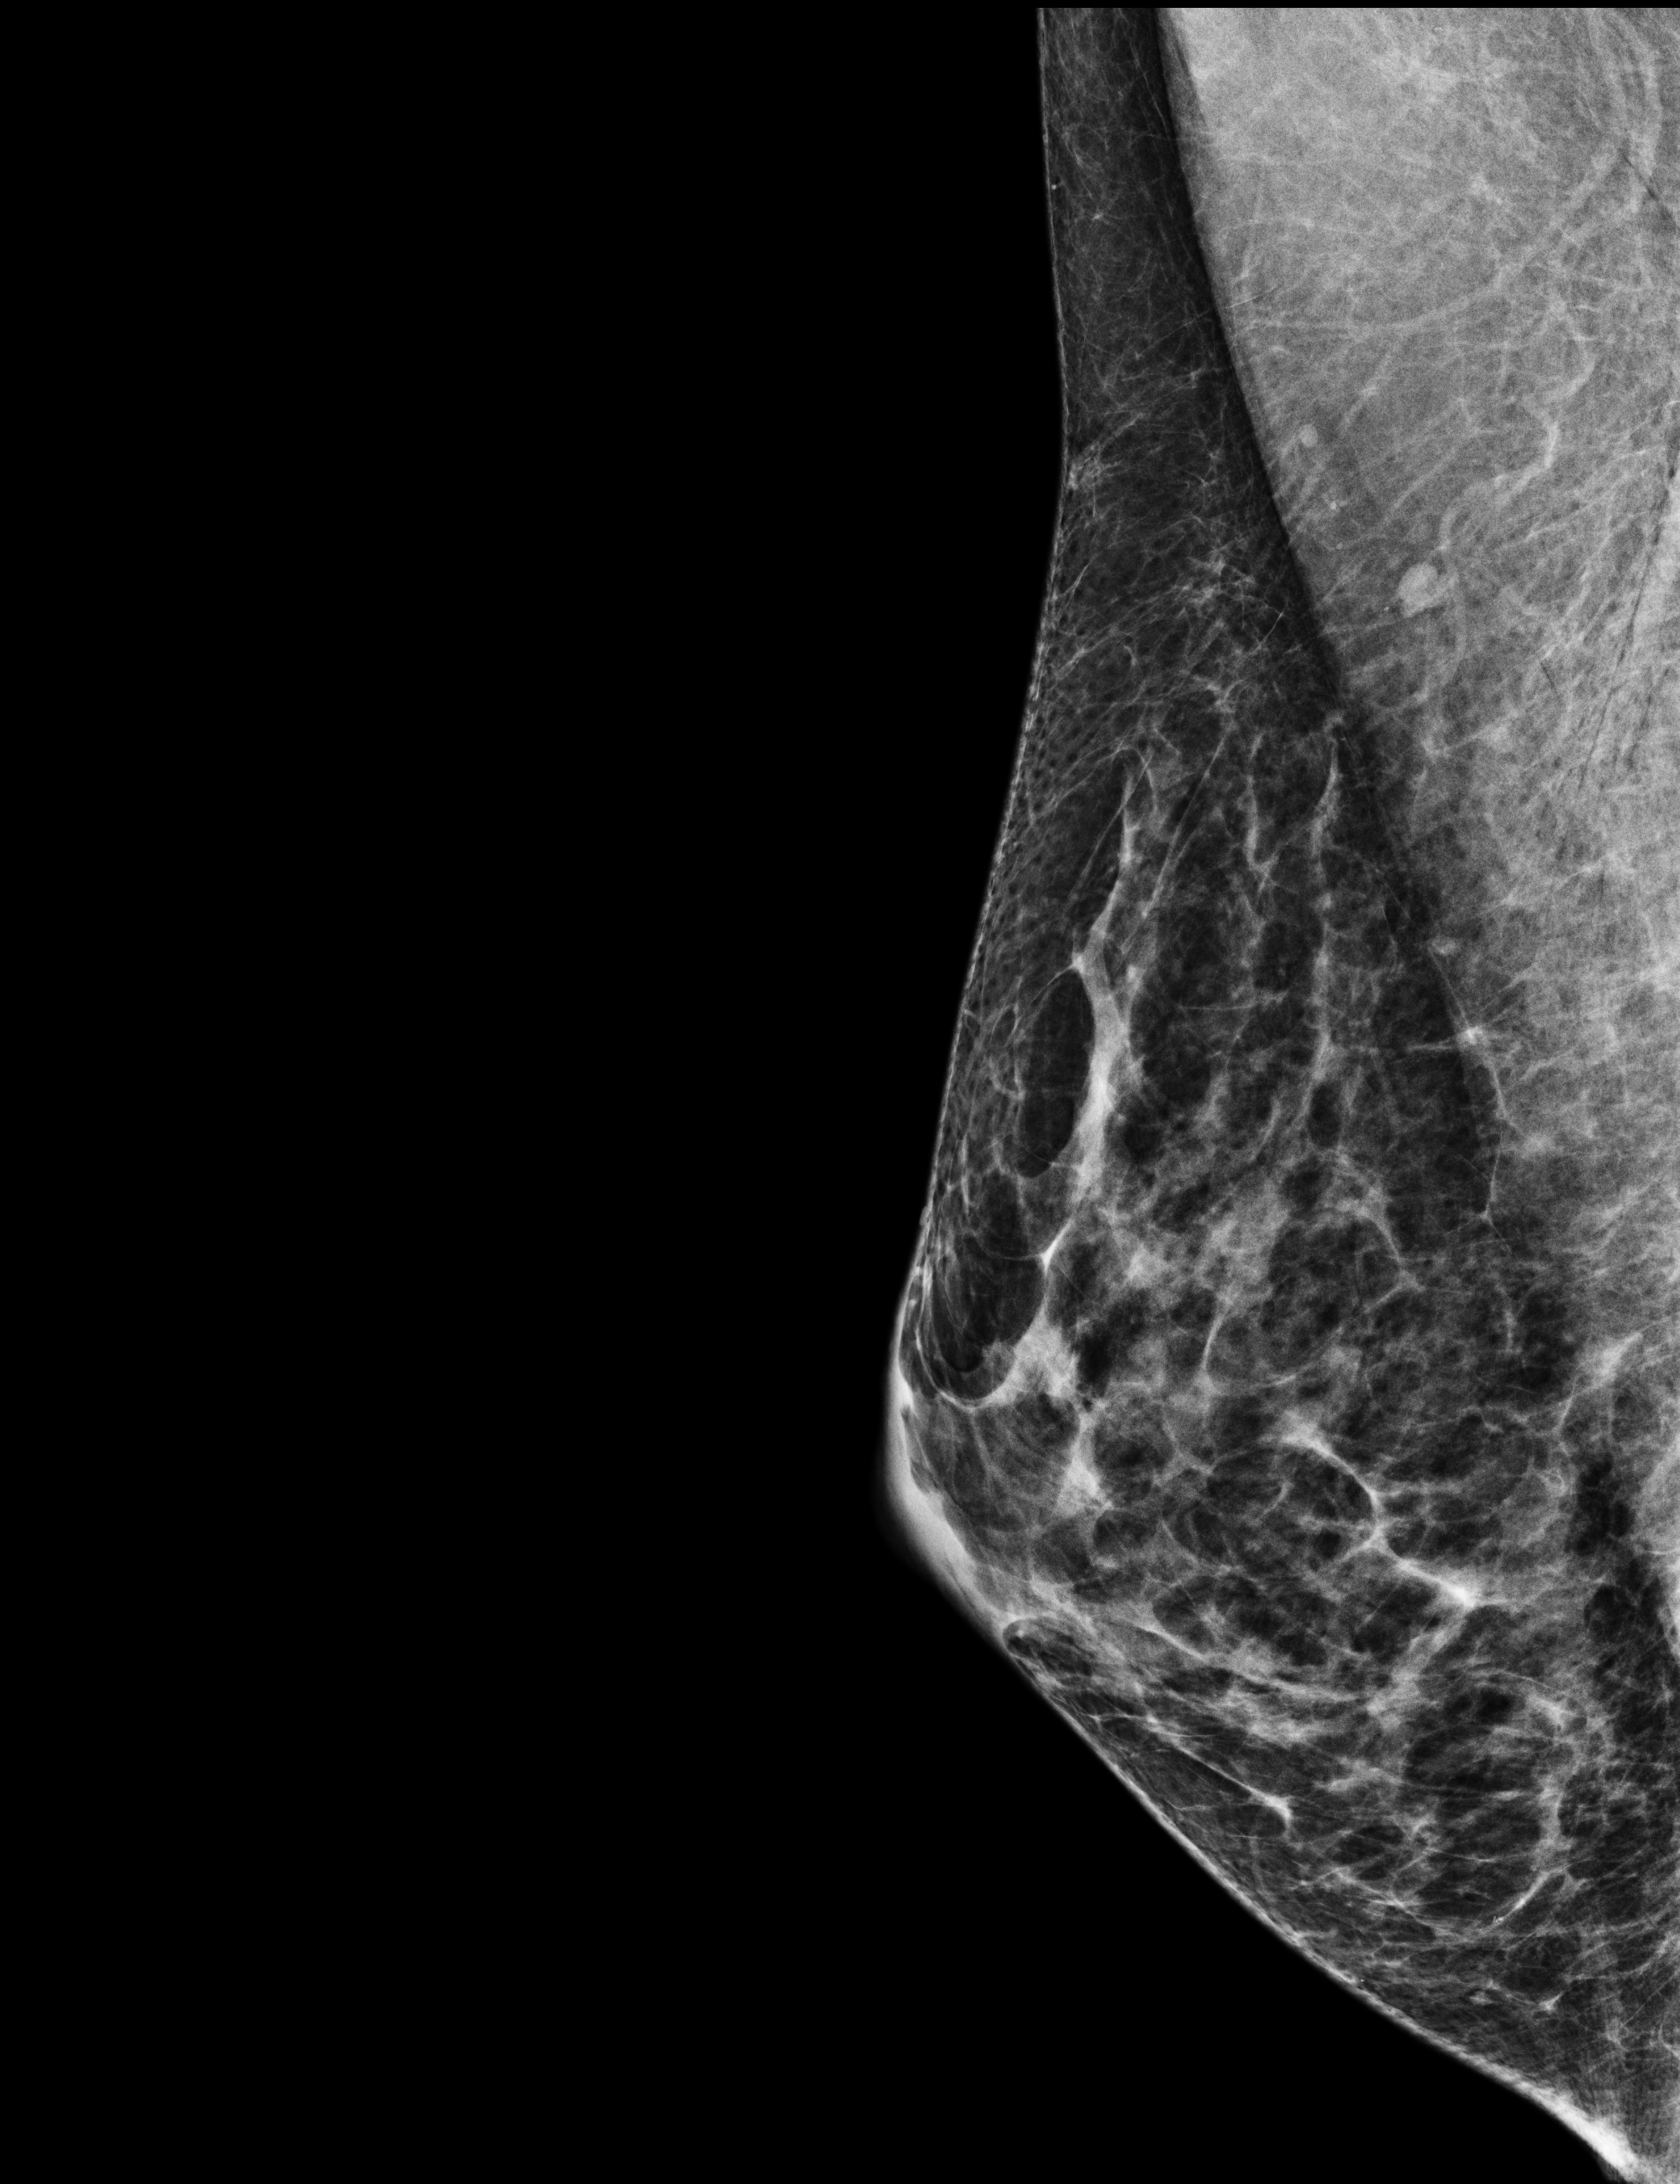
Annual screening mammography examination, compressed breast thickness 44 mm.
Image type: full-field digital mammogram. Breast: right. Projection: MLO view.